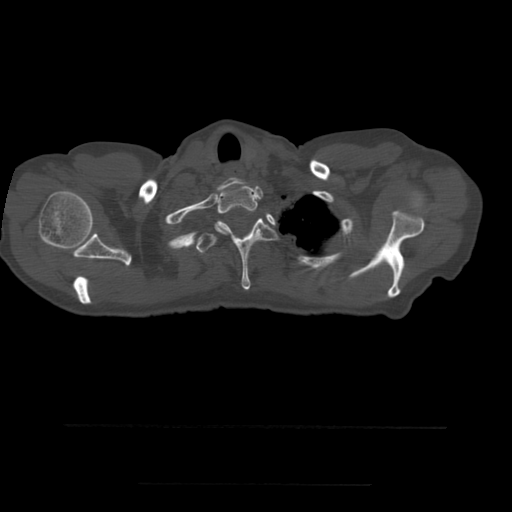
CT including the spine, one axial slice; position 440 of 544 along the scan axis; bone window (W 1800 / L 400 HU); 1.25 mm slice thickness; 512 × 512 image matrix. Patient age 58 years. Case-level facts recorded for this patient, not image findings: primary cancer: lung.
Outlined on this slice (semi-automatically segmented with operator editing):
- T1 vertebra: bounding box (x1, y1, x2, y2) in pixels: (216, 184, 258, 234)
- T2 vertebra: (196, 218, 278, 290)